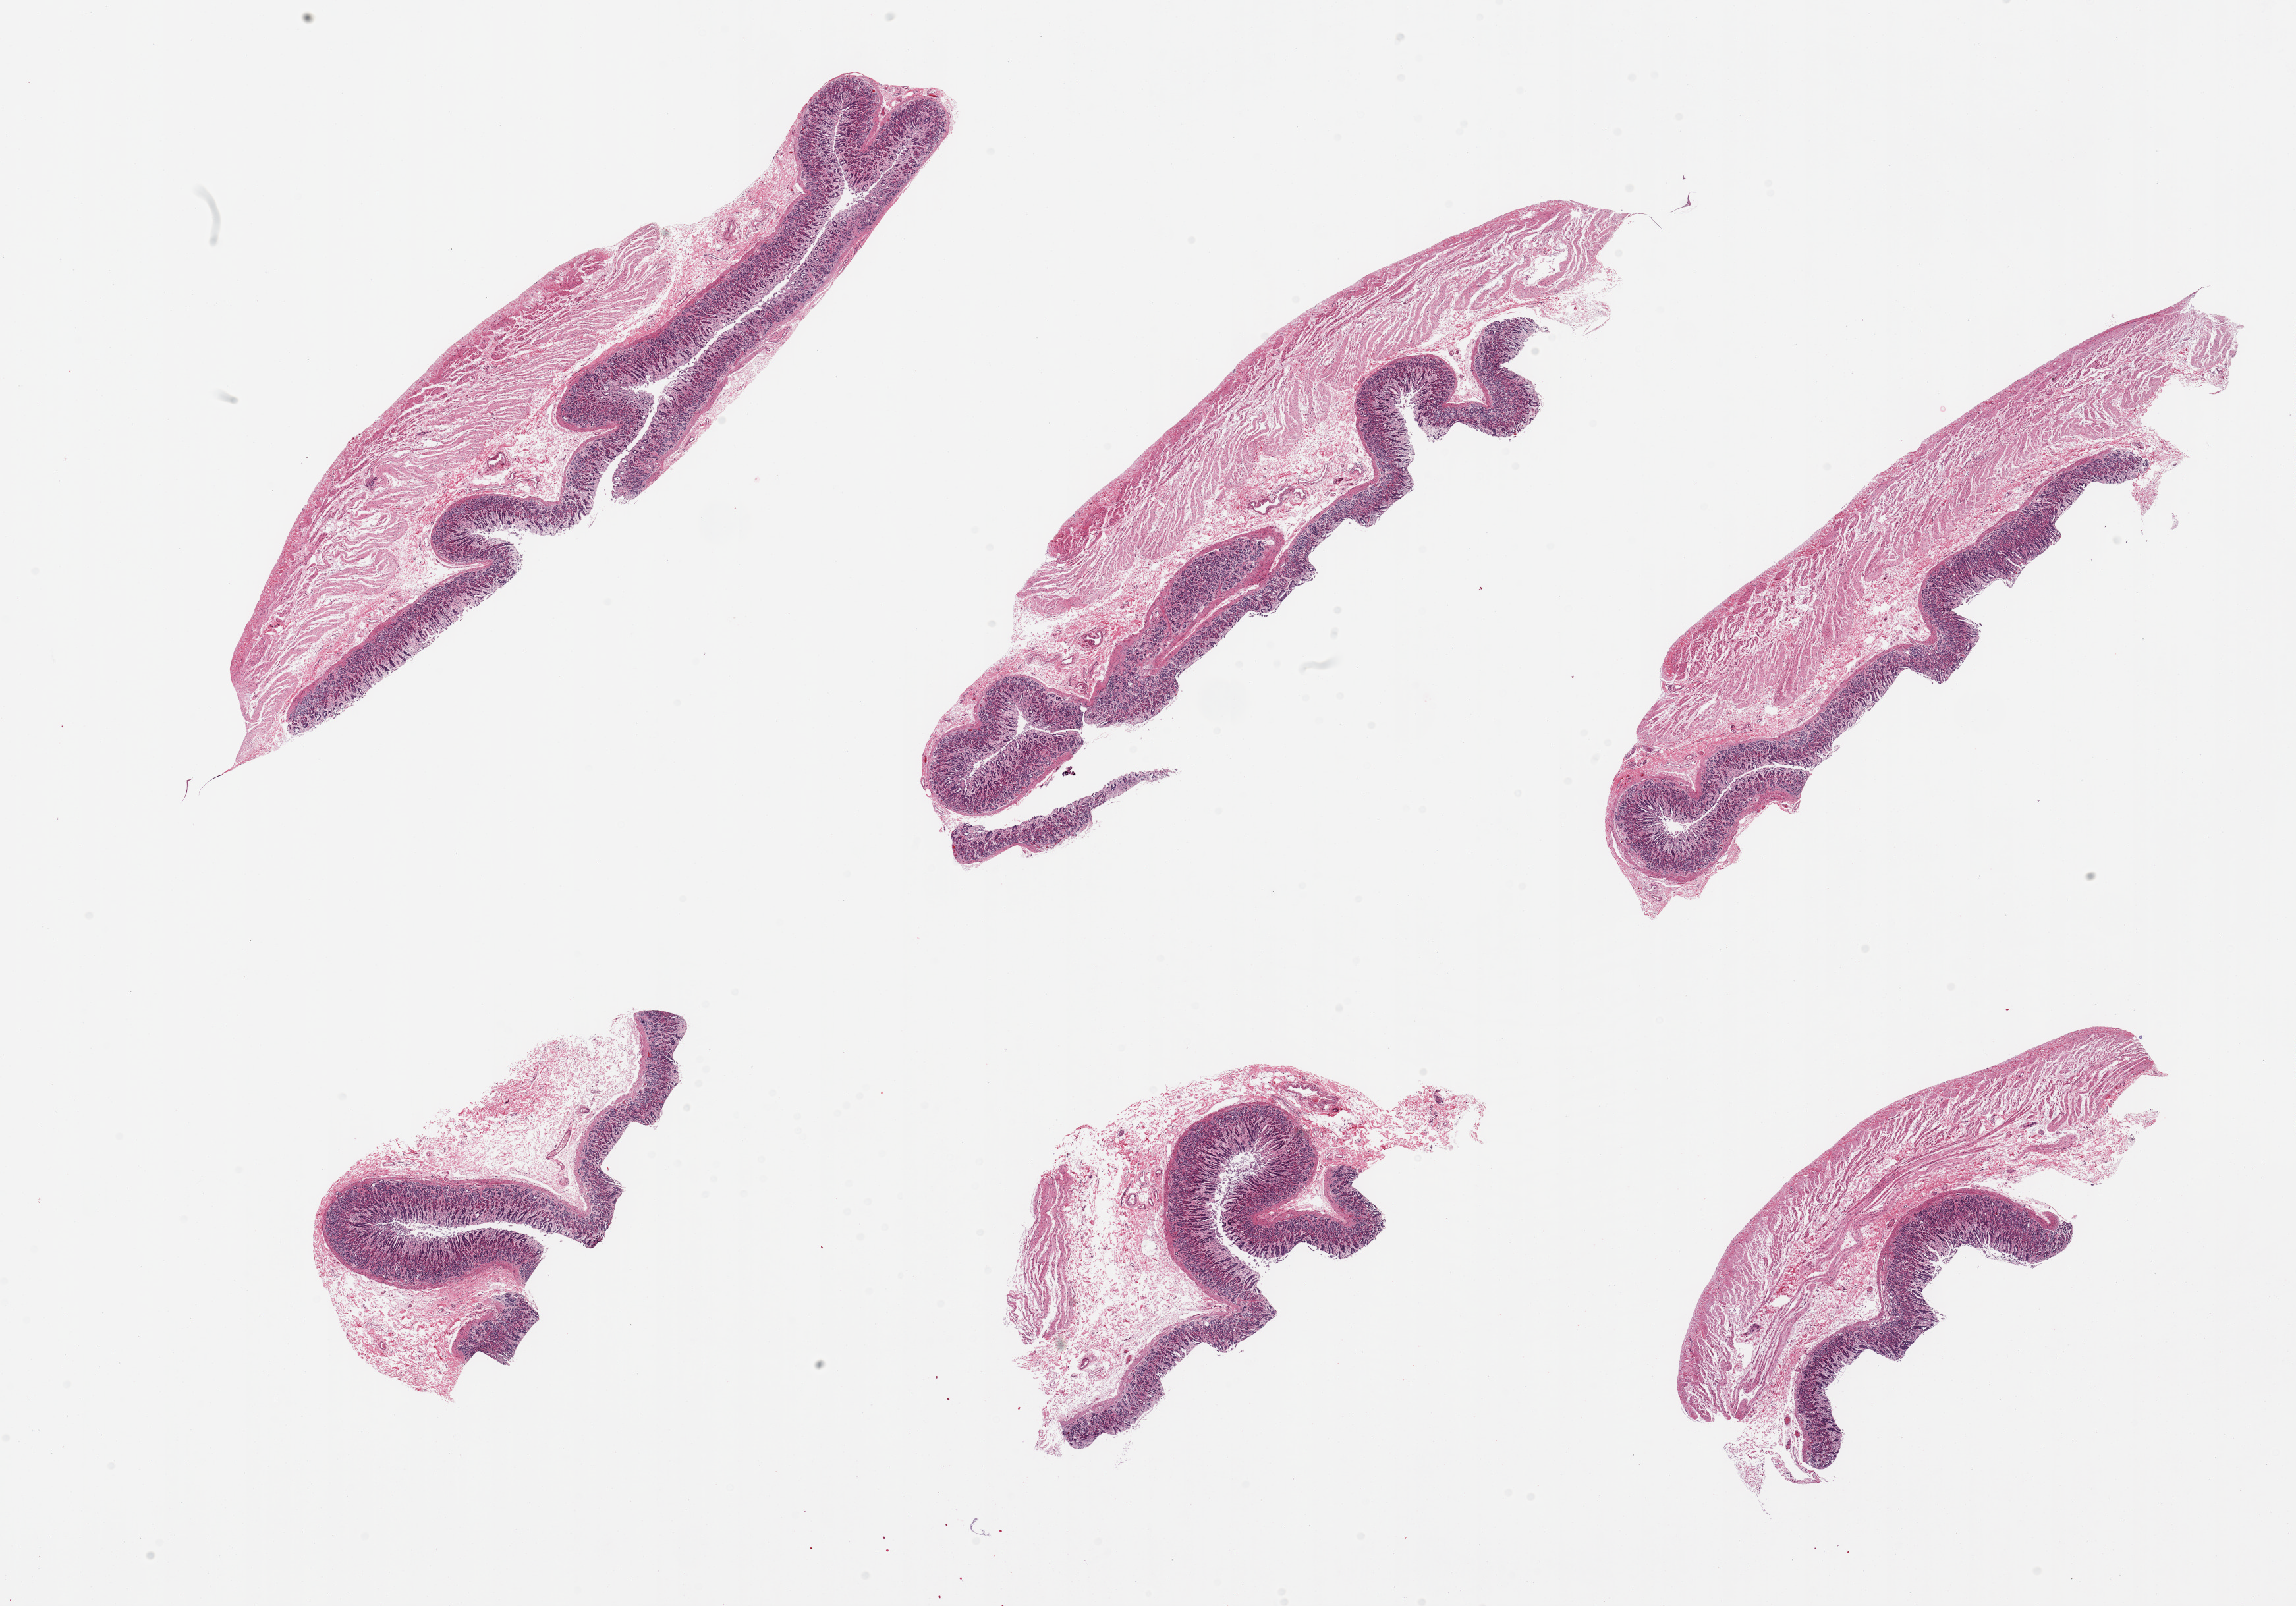
Hematoxylin and eosin (H&E) whole-slide image, shown as a low-resolution overview of the whole scanned area (about 27.6 x 19.3 mm); PAXgene-fixed paraffin-embedded (PFPE) section; sampled site (target tissue): stomach; donor tissue sample.
• pathologist's review note for this sample: 6 pieces; superficial half of mucosa autolyzed; 2 of 6 have little or no muscularis propria